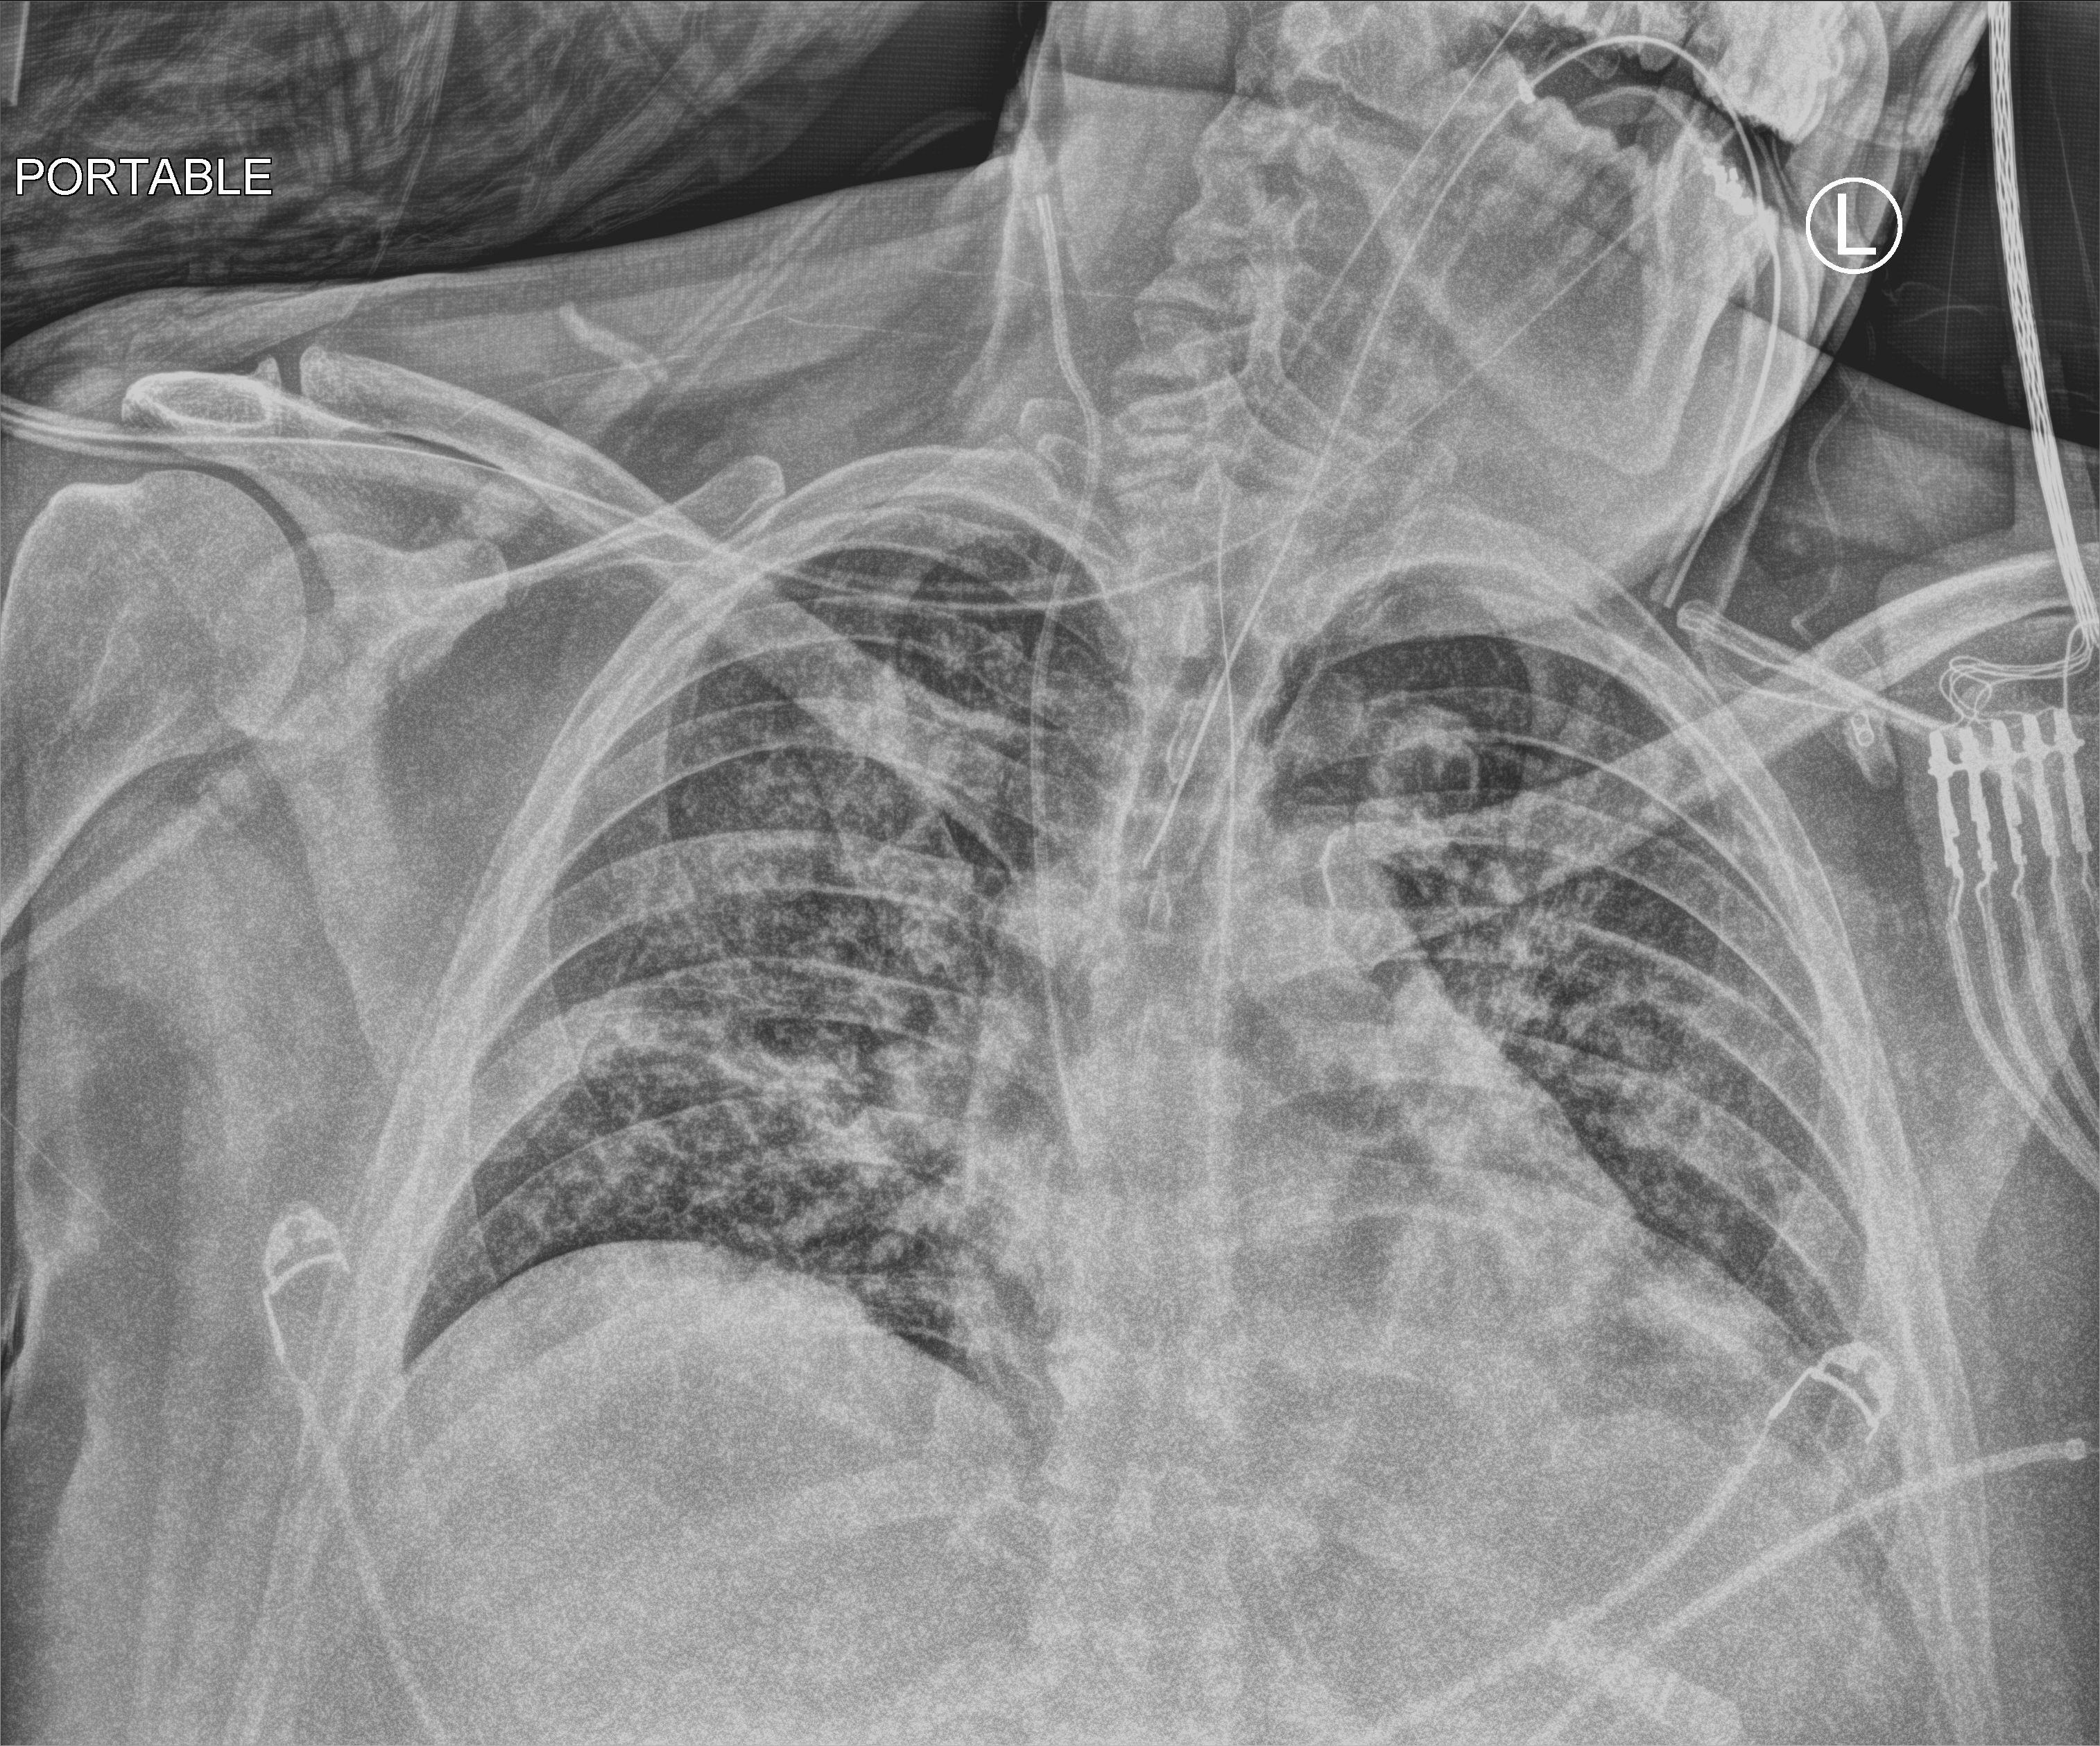
Chest X-ray (portable), anteroposterior (AP) projection. Patient hospitalised with COVID-19; male, aged 18–59 years.
From the hospital-stay record, not from the radiograph (when in the stay this image was taken is not recorded):
- mechanically ventilated during this hospital stay: yes
- length of hospital stay: 39 days